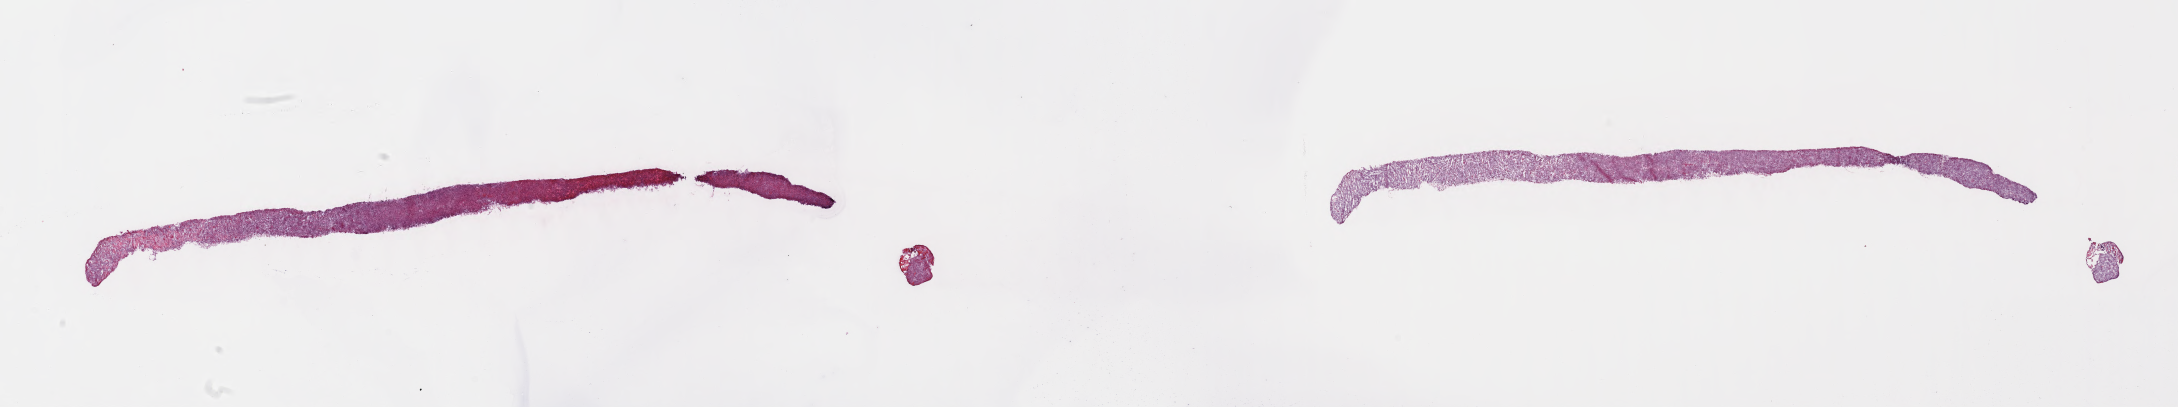
Digitized H&E-stained section, shown as a low-resolution overview of the whole scanned area (about 35.2 x 6.6 mm), frozen section, primary tumor, anatomic site: ovary. Female, age 9 years at initial diagnosis. Slide review estimates, as recorded: tumor cells 90%, tumor nuclei 95%, stromal cells 5%, necrosis 5%, normal cells 0%. Infiltration values recorded for this section: lymphocyte infiltration 35%, monocyte infiltration 20%, neutrophil infiltration 5%.
Ann Arbor stage (patient): Stage III. Diagnosis: Burkitt lymphoma, NOS.